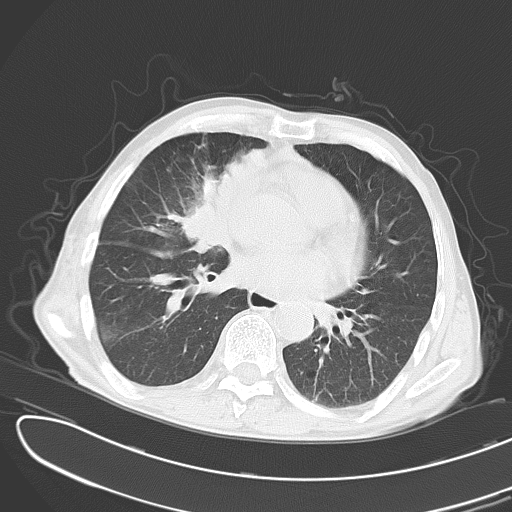
Chest CT, one axial slice. Slice 14 of 43 in the series (ordered by position). Reconstruction kernel B70f. 120 kVp. Lung window (W 1500 / L -600 HU). 5 mm slice thickness. 512 × 512 image matrix, field of view 353 × 353 mm. Male patient, age 65 years. From the clinical record (not read from this slice): clinical TNM (as recorded): T2 N3 M1.
Outlined on this slice (bounding box drawn by a radiologist):
- lung tumour (recorded histology: small cell carcinoma): bounding box (x1, y1, x2, y2) in pixels: (169, 144, 271, 254)